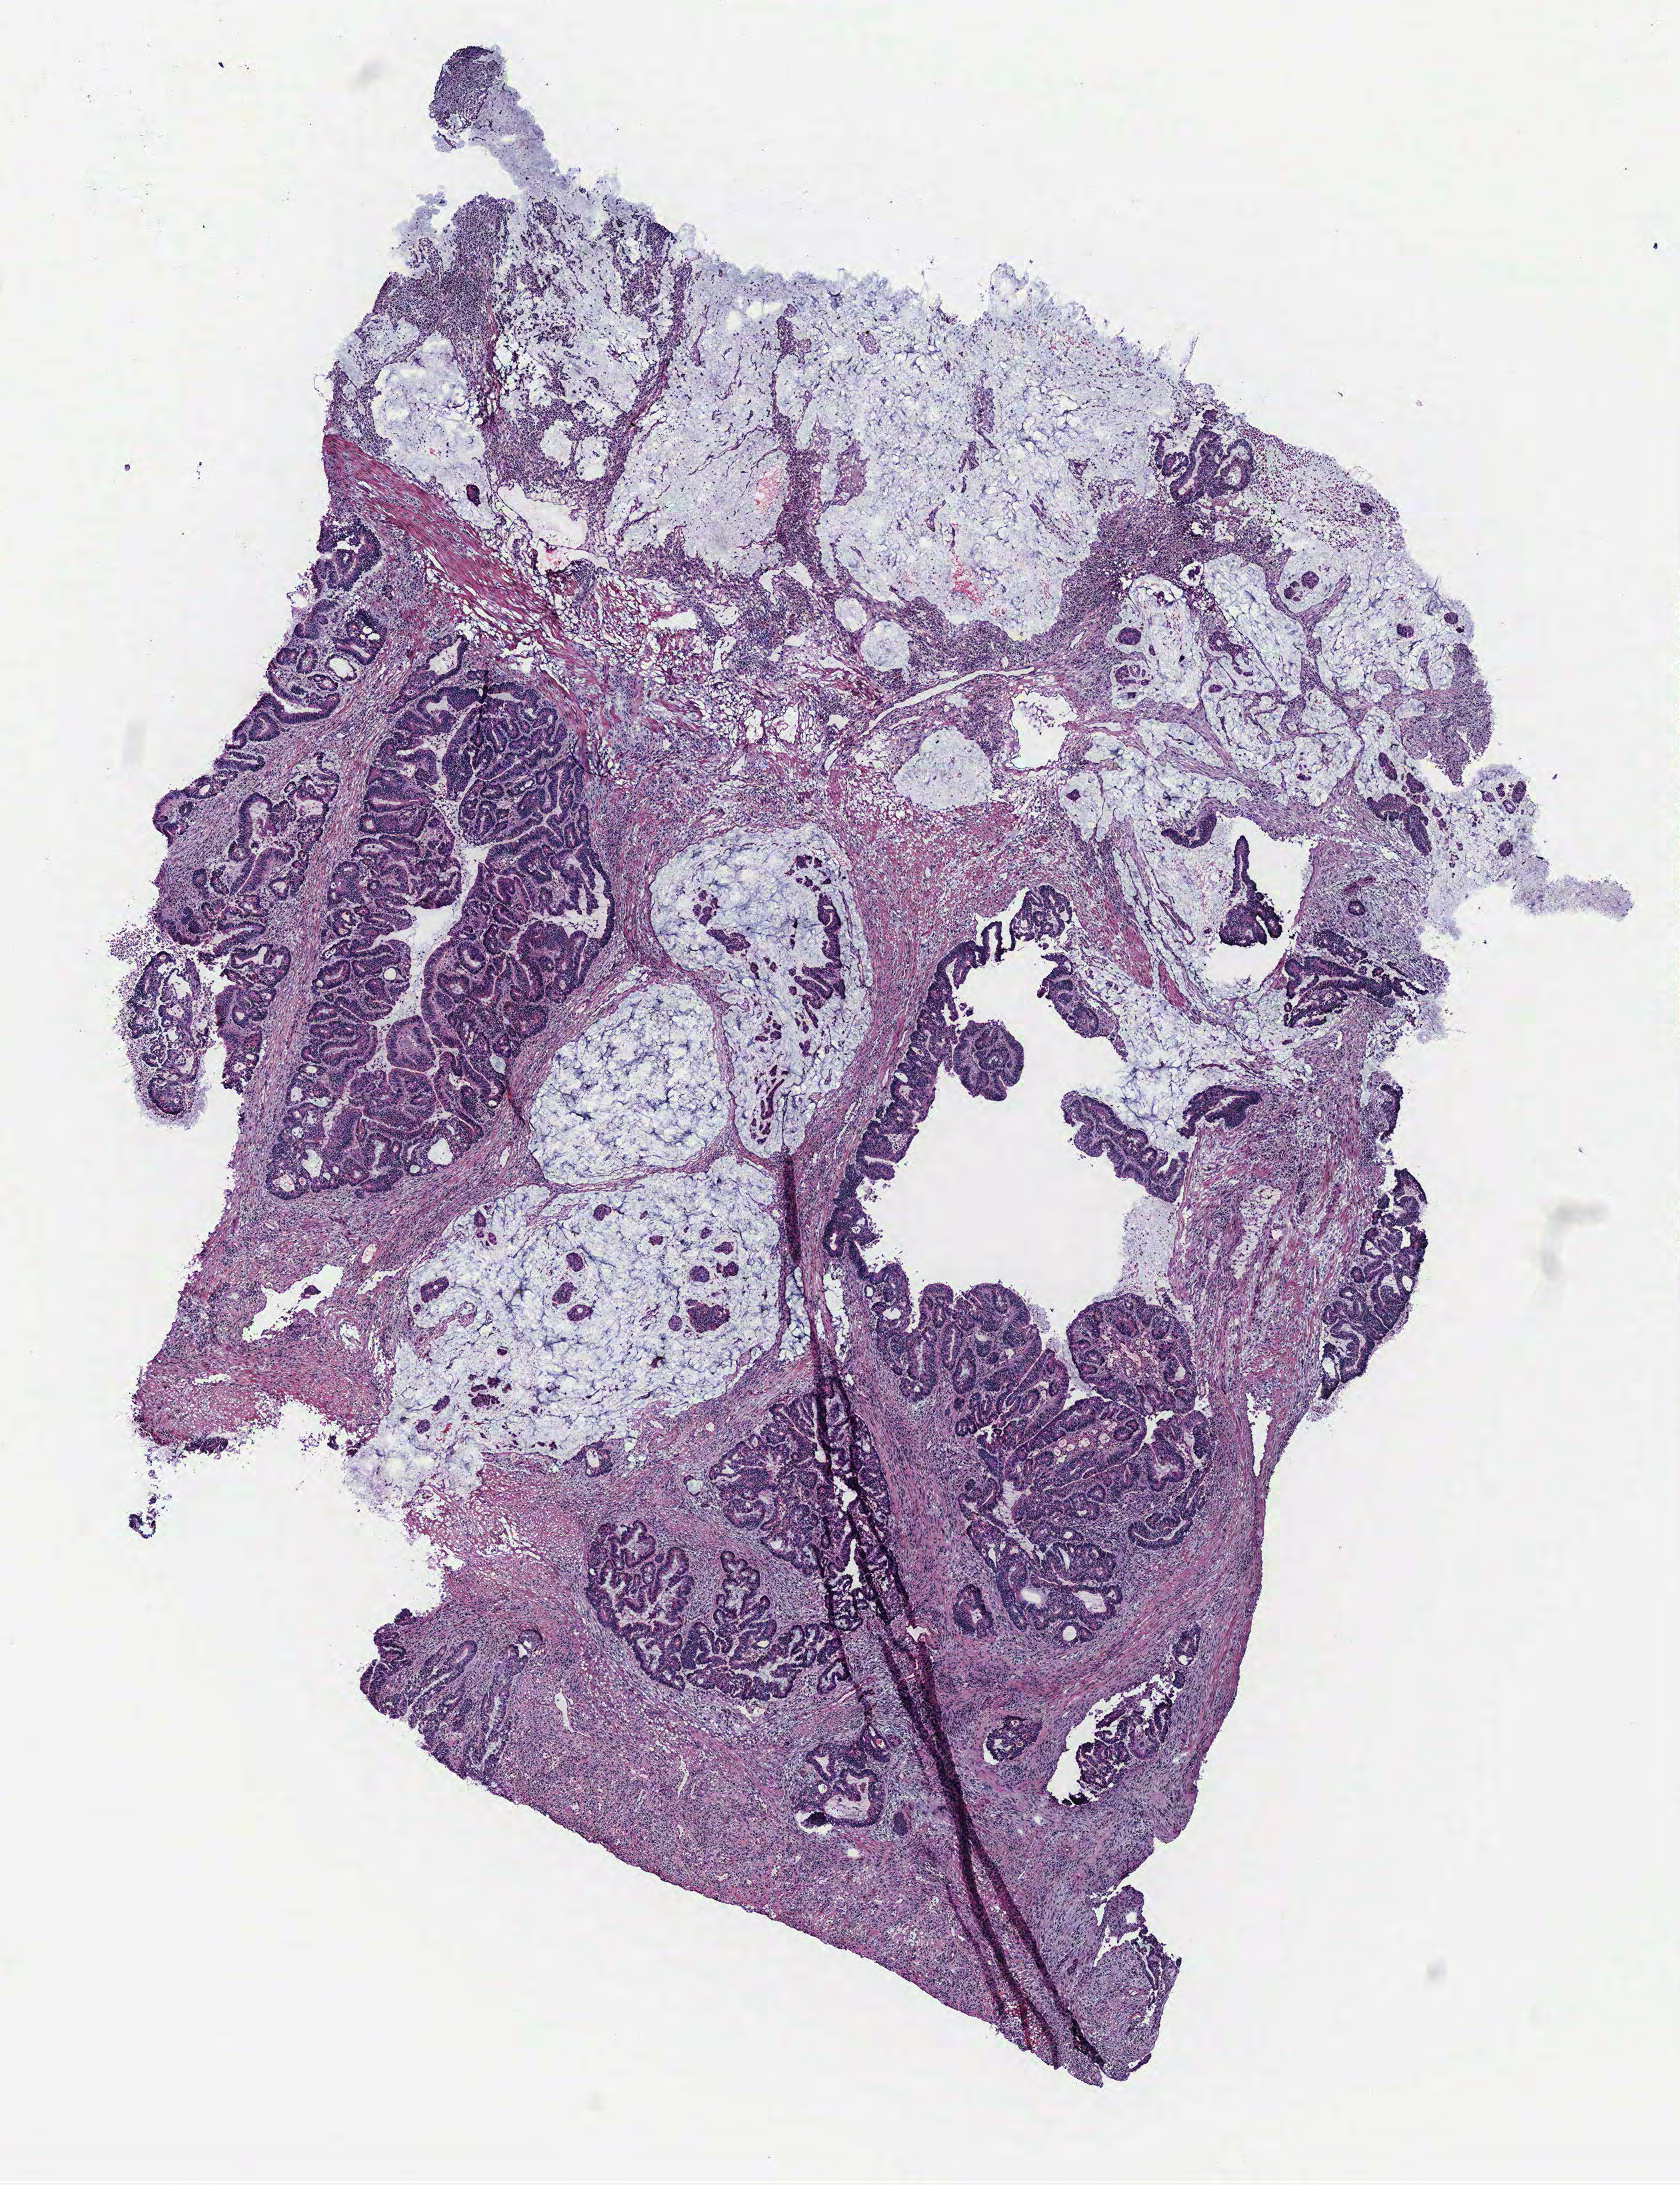
Digitized Hematoxylin and eosin (H&E) stained tissue section (whole slide), shown as a low-resolution overview of the whole scanned area (about 6.7 x 8.7 mm, acquisition: 40x scan); colon, tissue type not recorded. Female patient.
* patient diagnosis: Adenocarcinoma, NOS